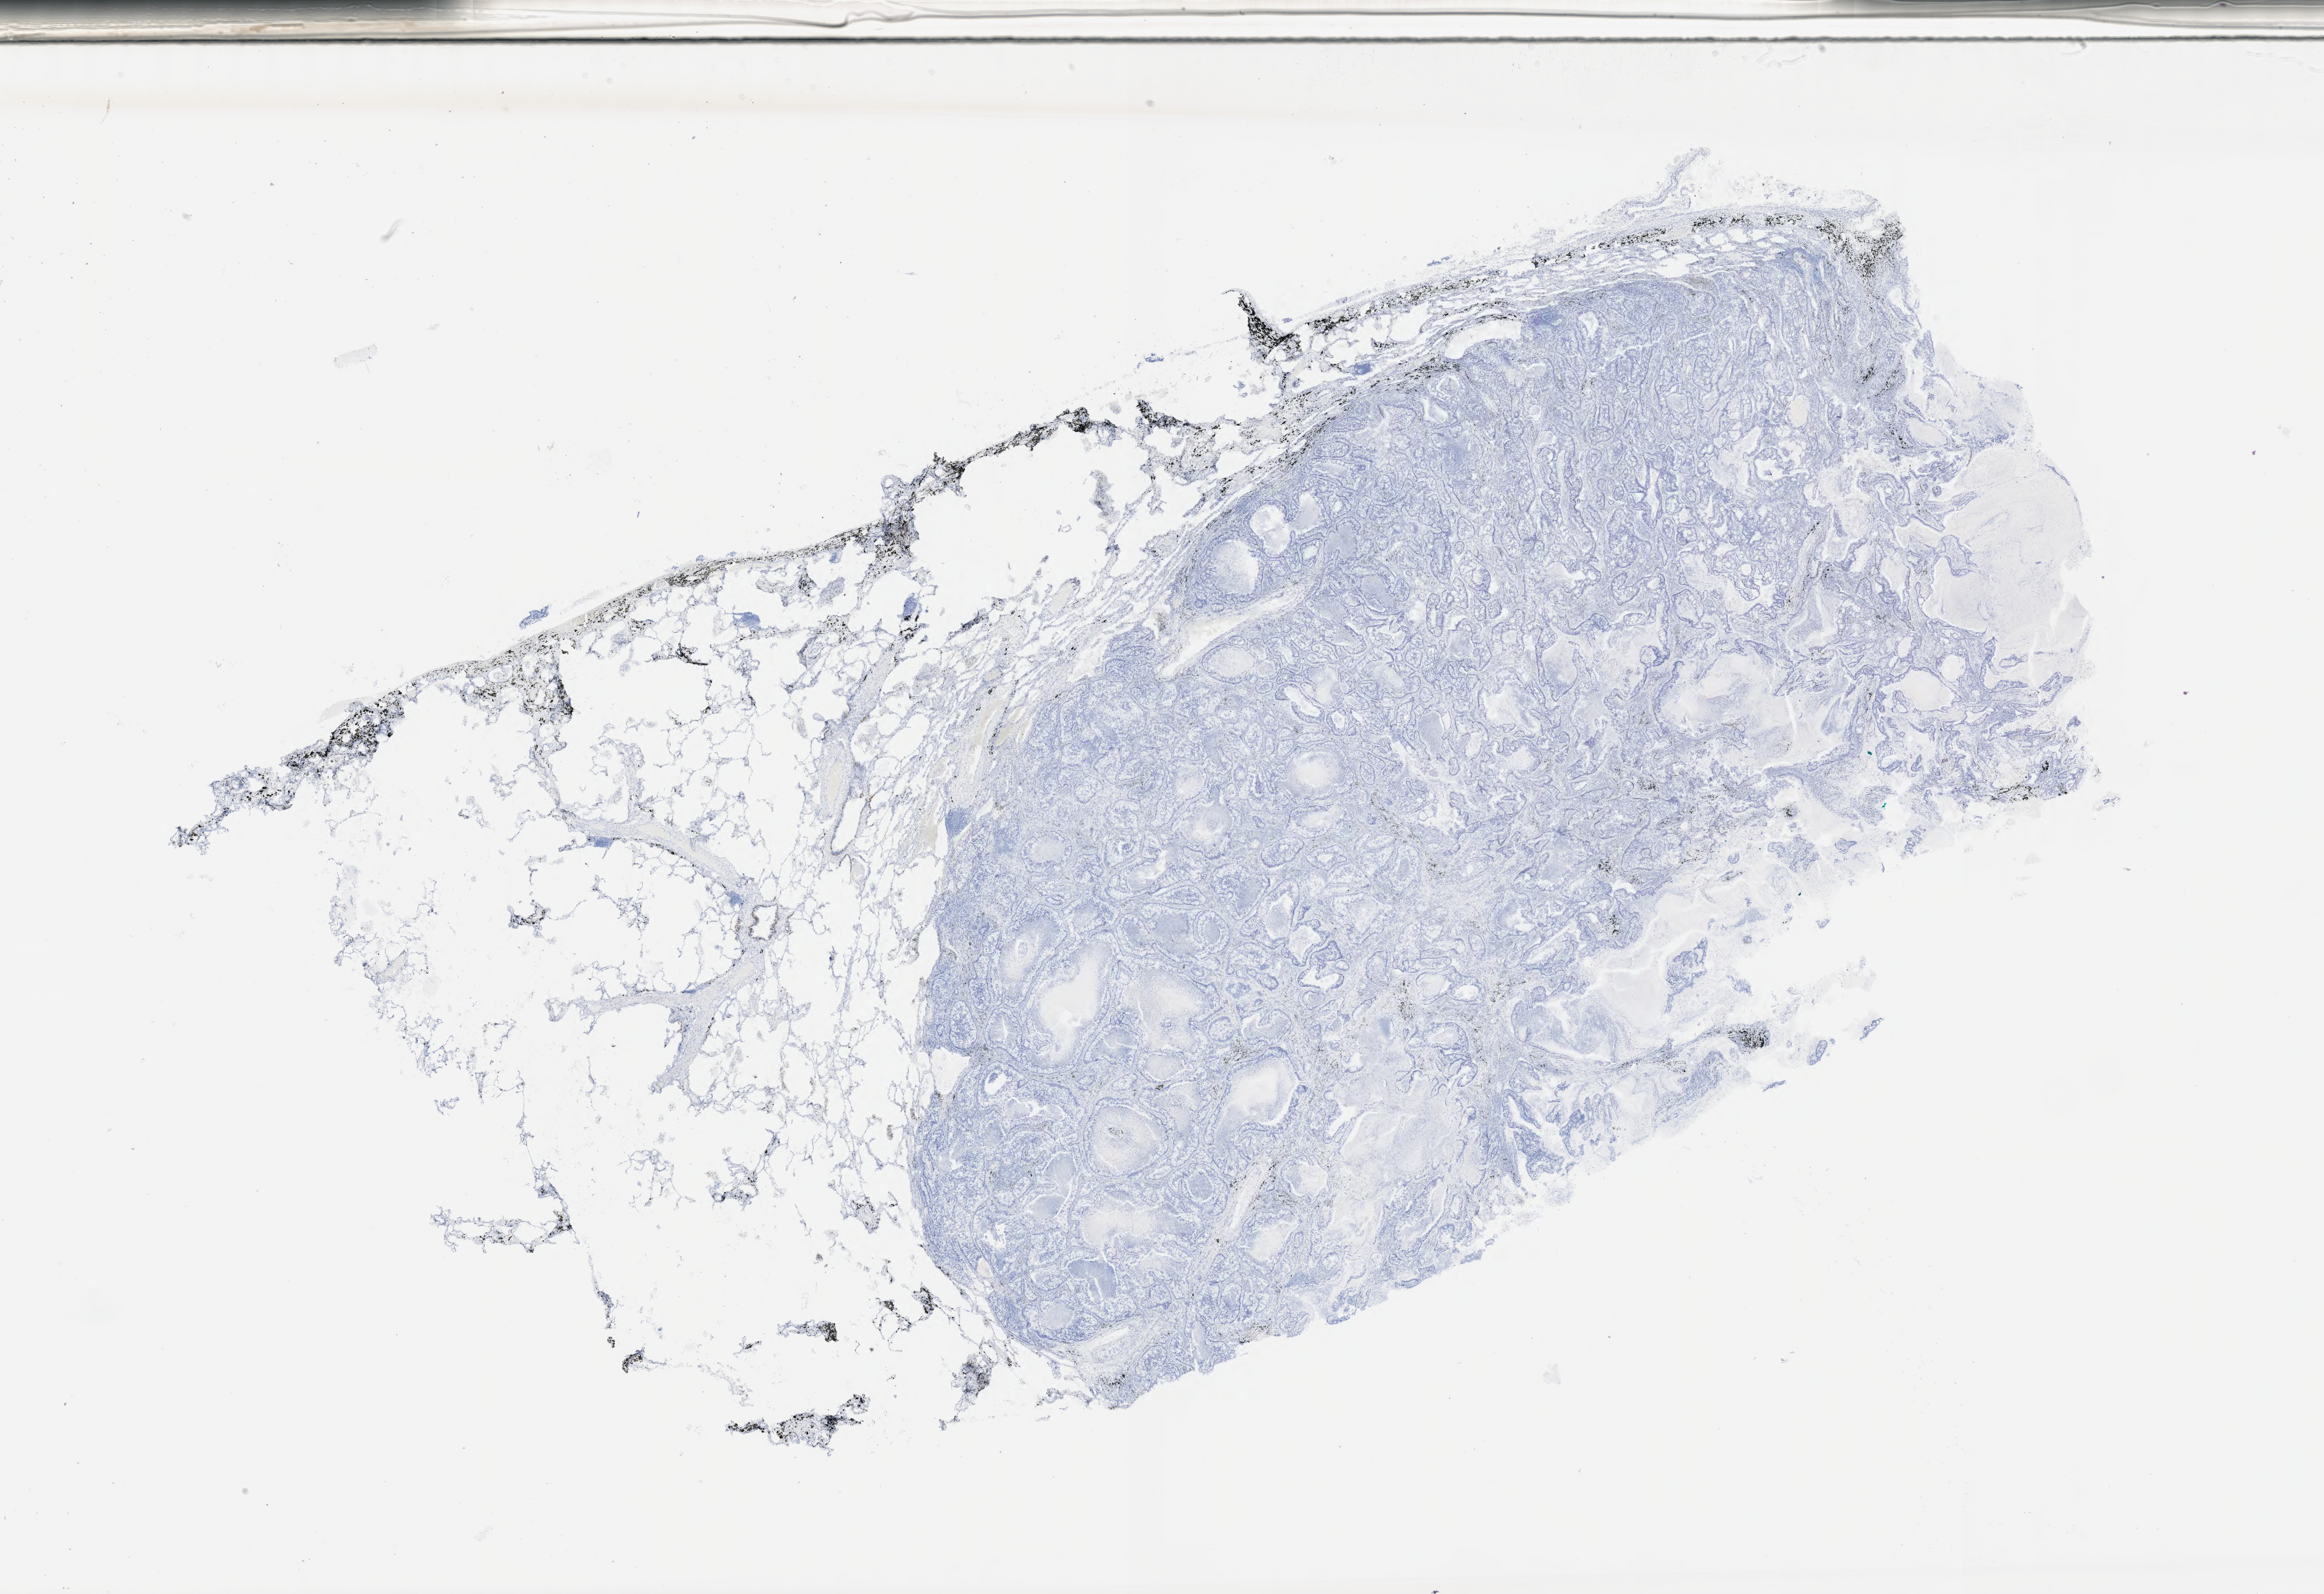
IHC for p40, whole-slide image — low-resolution overview of the scanned area, about 32.2 x 22.1 mm, specimen: tumor tissue, anatomic site: lung. Patient sex: female.
Diagnosis: Adenocarcinoma, NOS.